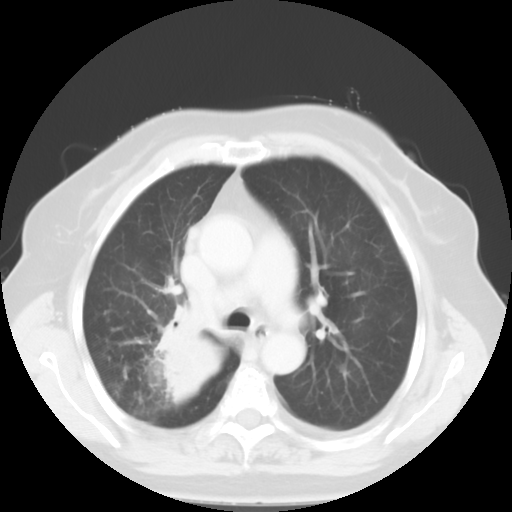
Chest CT, one axial slice; slice 35 of 52 in the series (ordered by position); lung window (W 1500 / L -600 HU); 5 mm slice thickness; 512 × 512 image matrix. Female patient, age 81 years. Case-level facts recorded for this patient, not image findings: clinical TNM (as recorded): T4 N3 M1b.
Structures marked on this image (rectangle marked by the reading radiologist):
- lung tumour (recorded histology: adenocarcinoma): bounding box <152,306,219,404> (left, top, right, bottom; pixels)